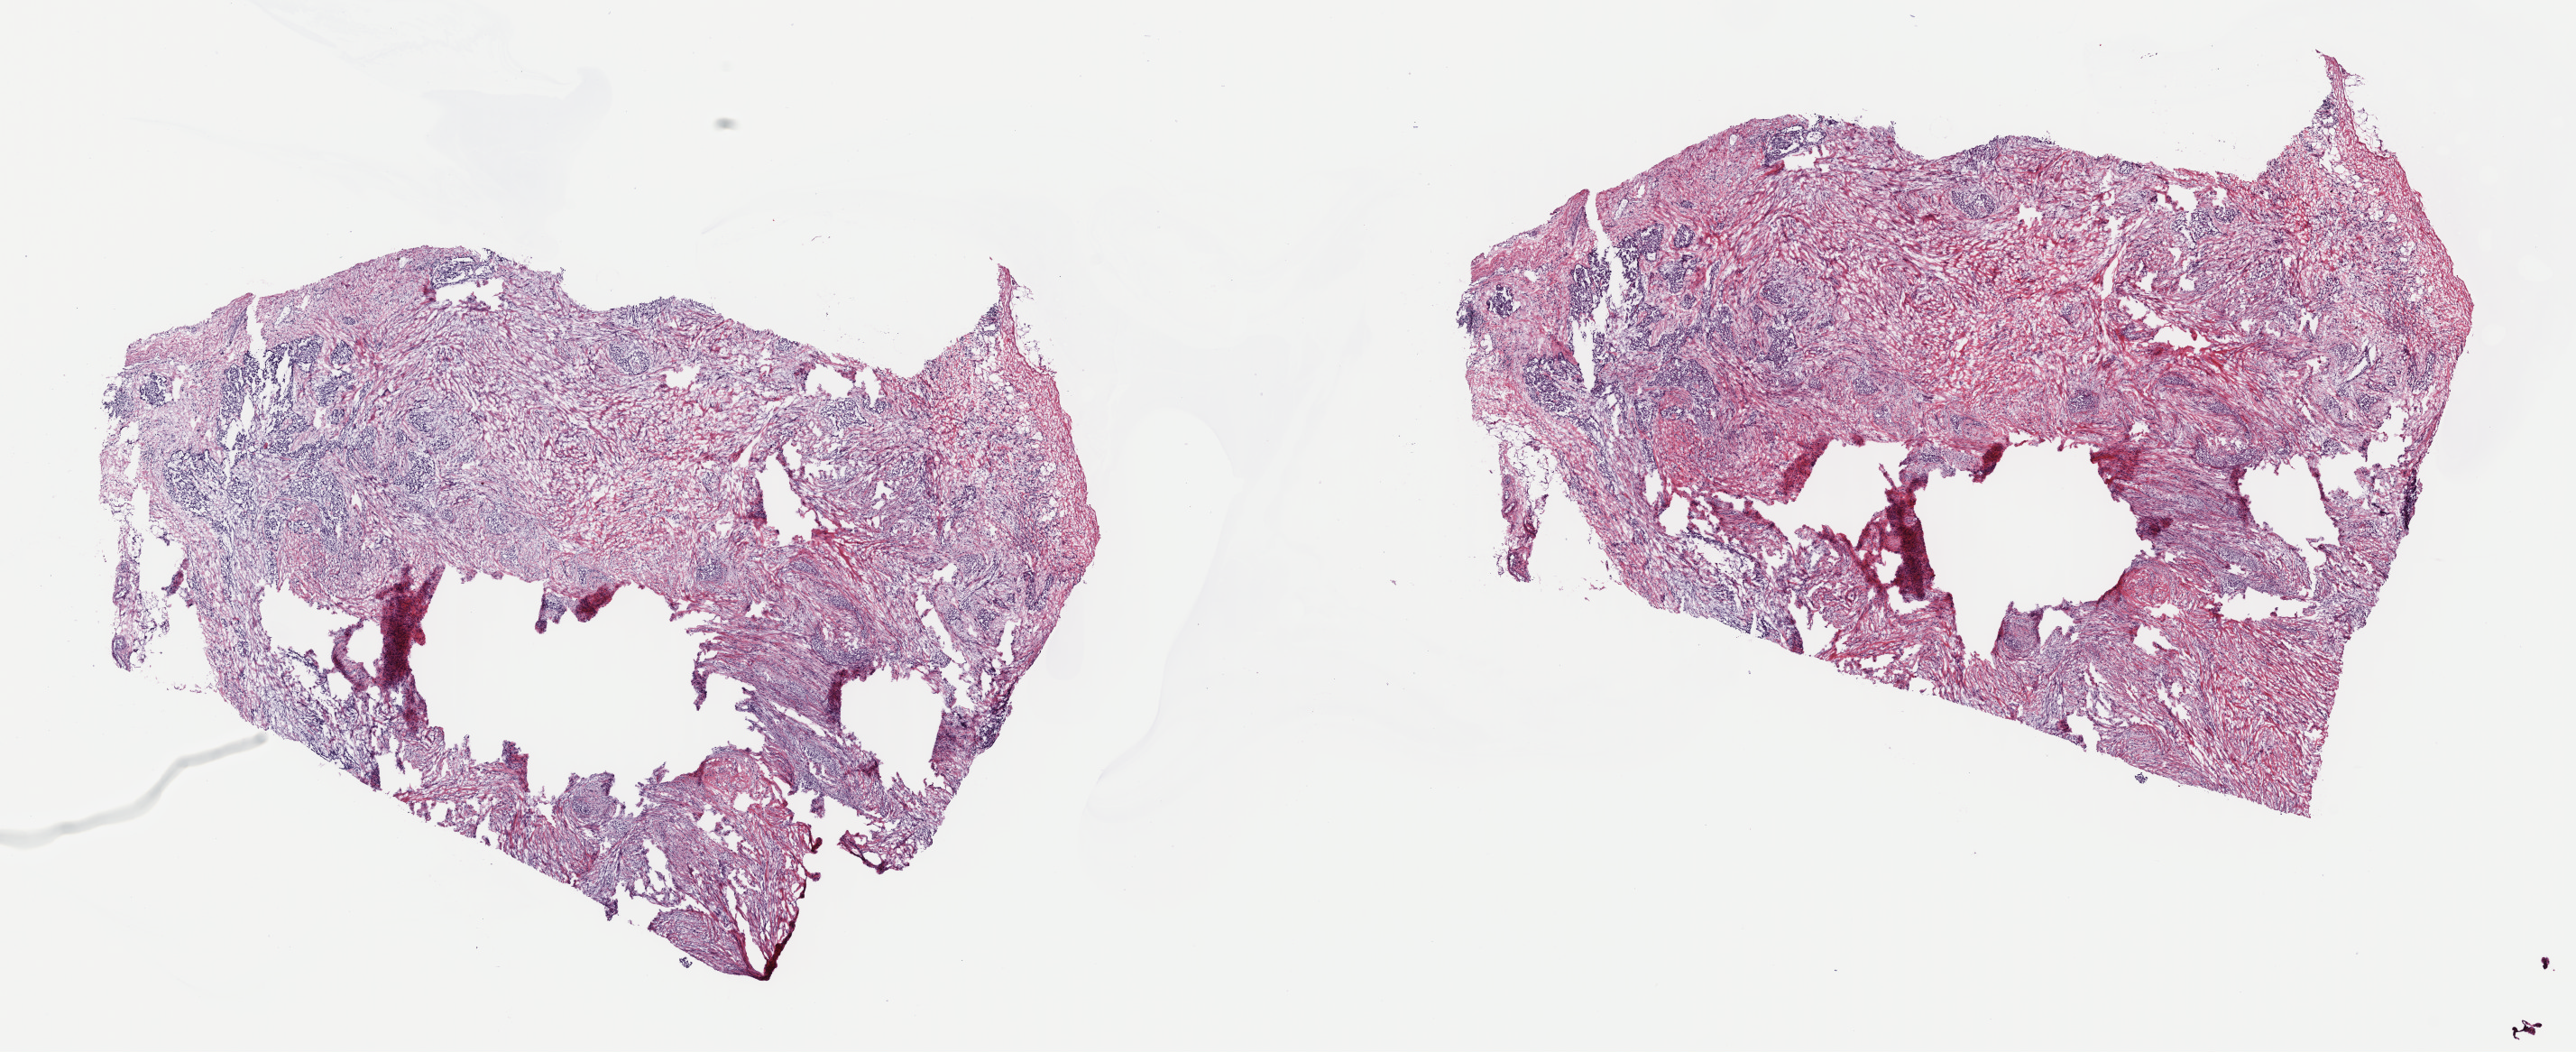
Digitized Hematoxylin and eosin (H&E) stained tissue section (whole slide), whole scanned area (about 22.5 x 9.2 mm, slide scanned at 40x) shown as a low-resolution overview. Frozen section from the top of the tissue portion. Mesothelium, primary tumour sample. Male patient; age at initial diagnosis 76 years. Composition of this section per pathologist review: tumour cells 100%, tumour nuclei 80%, normal cells 0%, stromal cells 0%, necrosis 0%. Infiltration values recorded for this section: lymphocyte infiltration 2%, monocyte infiltration 0%, neutrophil infiltration 0%.
- AJCC pathologic stage: III
- diagnosis: Mesothelioma, biphasic, malignant (pleura, NOS)